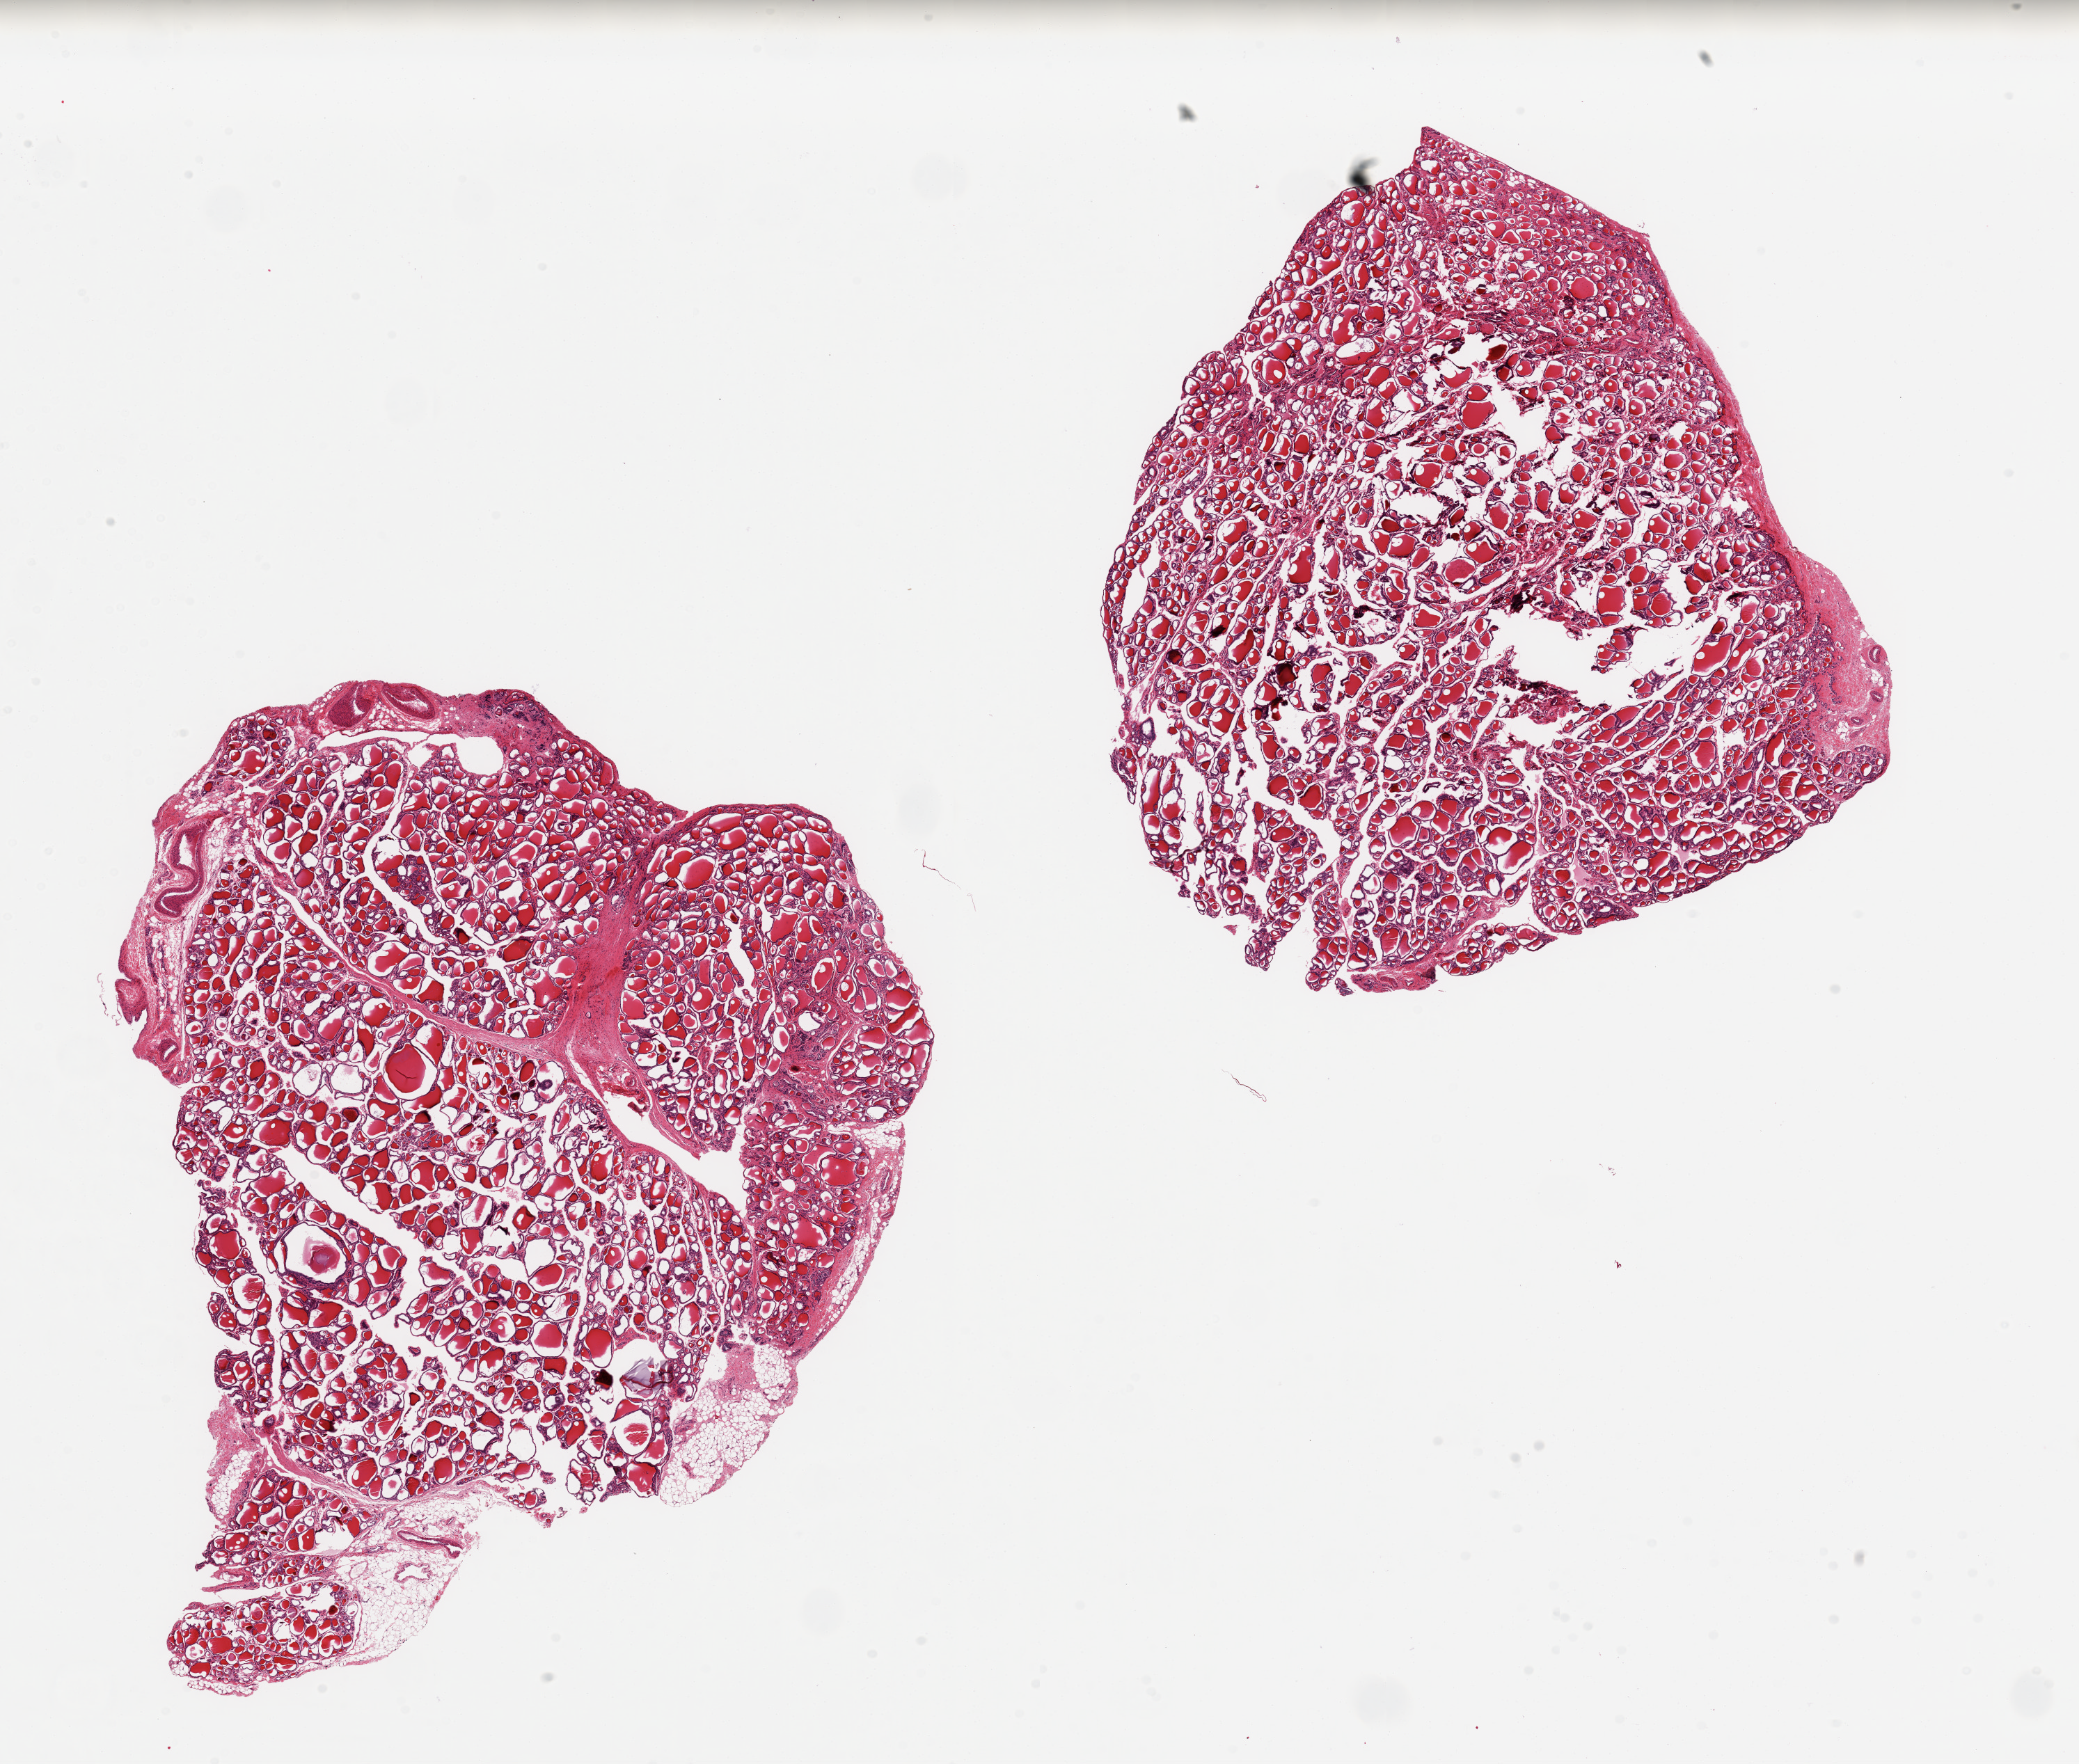
Hematoxylin and eosin (H&E) whole-slide image — low-resolution overview of the scanned area, about 23.6 x 20.1 mm (acquisition: 20x scan); PAXgene-fixed, paraffin-embedded tissue; section of thyroid (target tissue); donor tissue sample. Female donor.
Pathologist's review note for this sample: 2 pieces12x9 & 8x8 mm; <5% adipose.